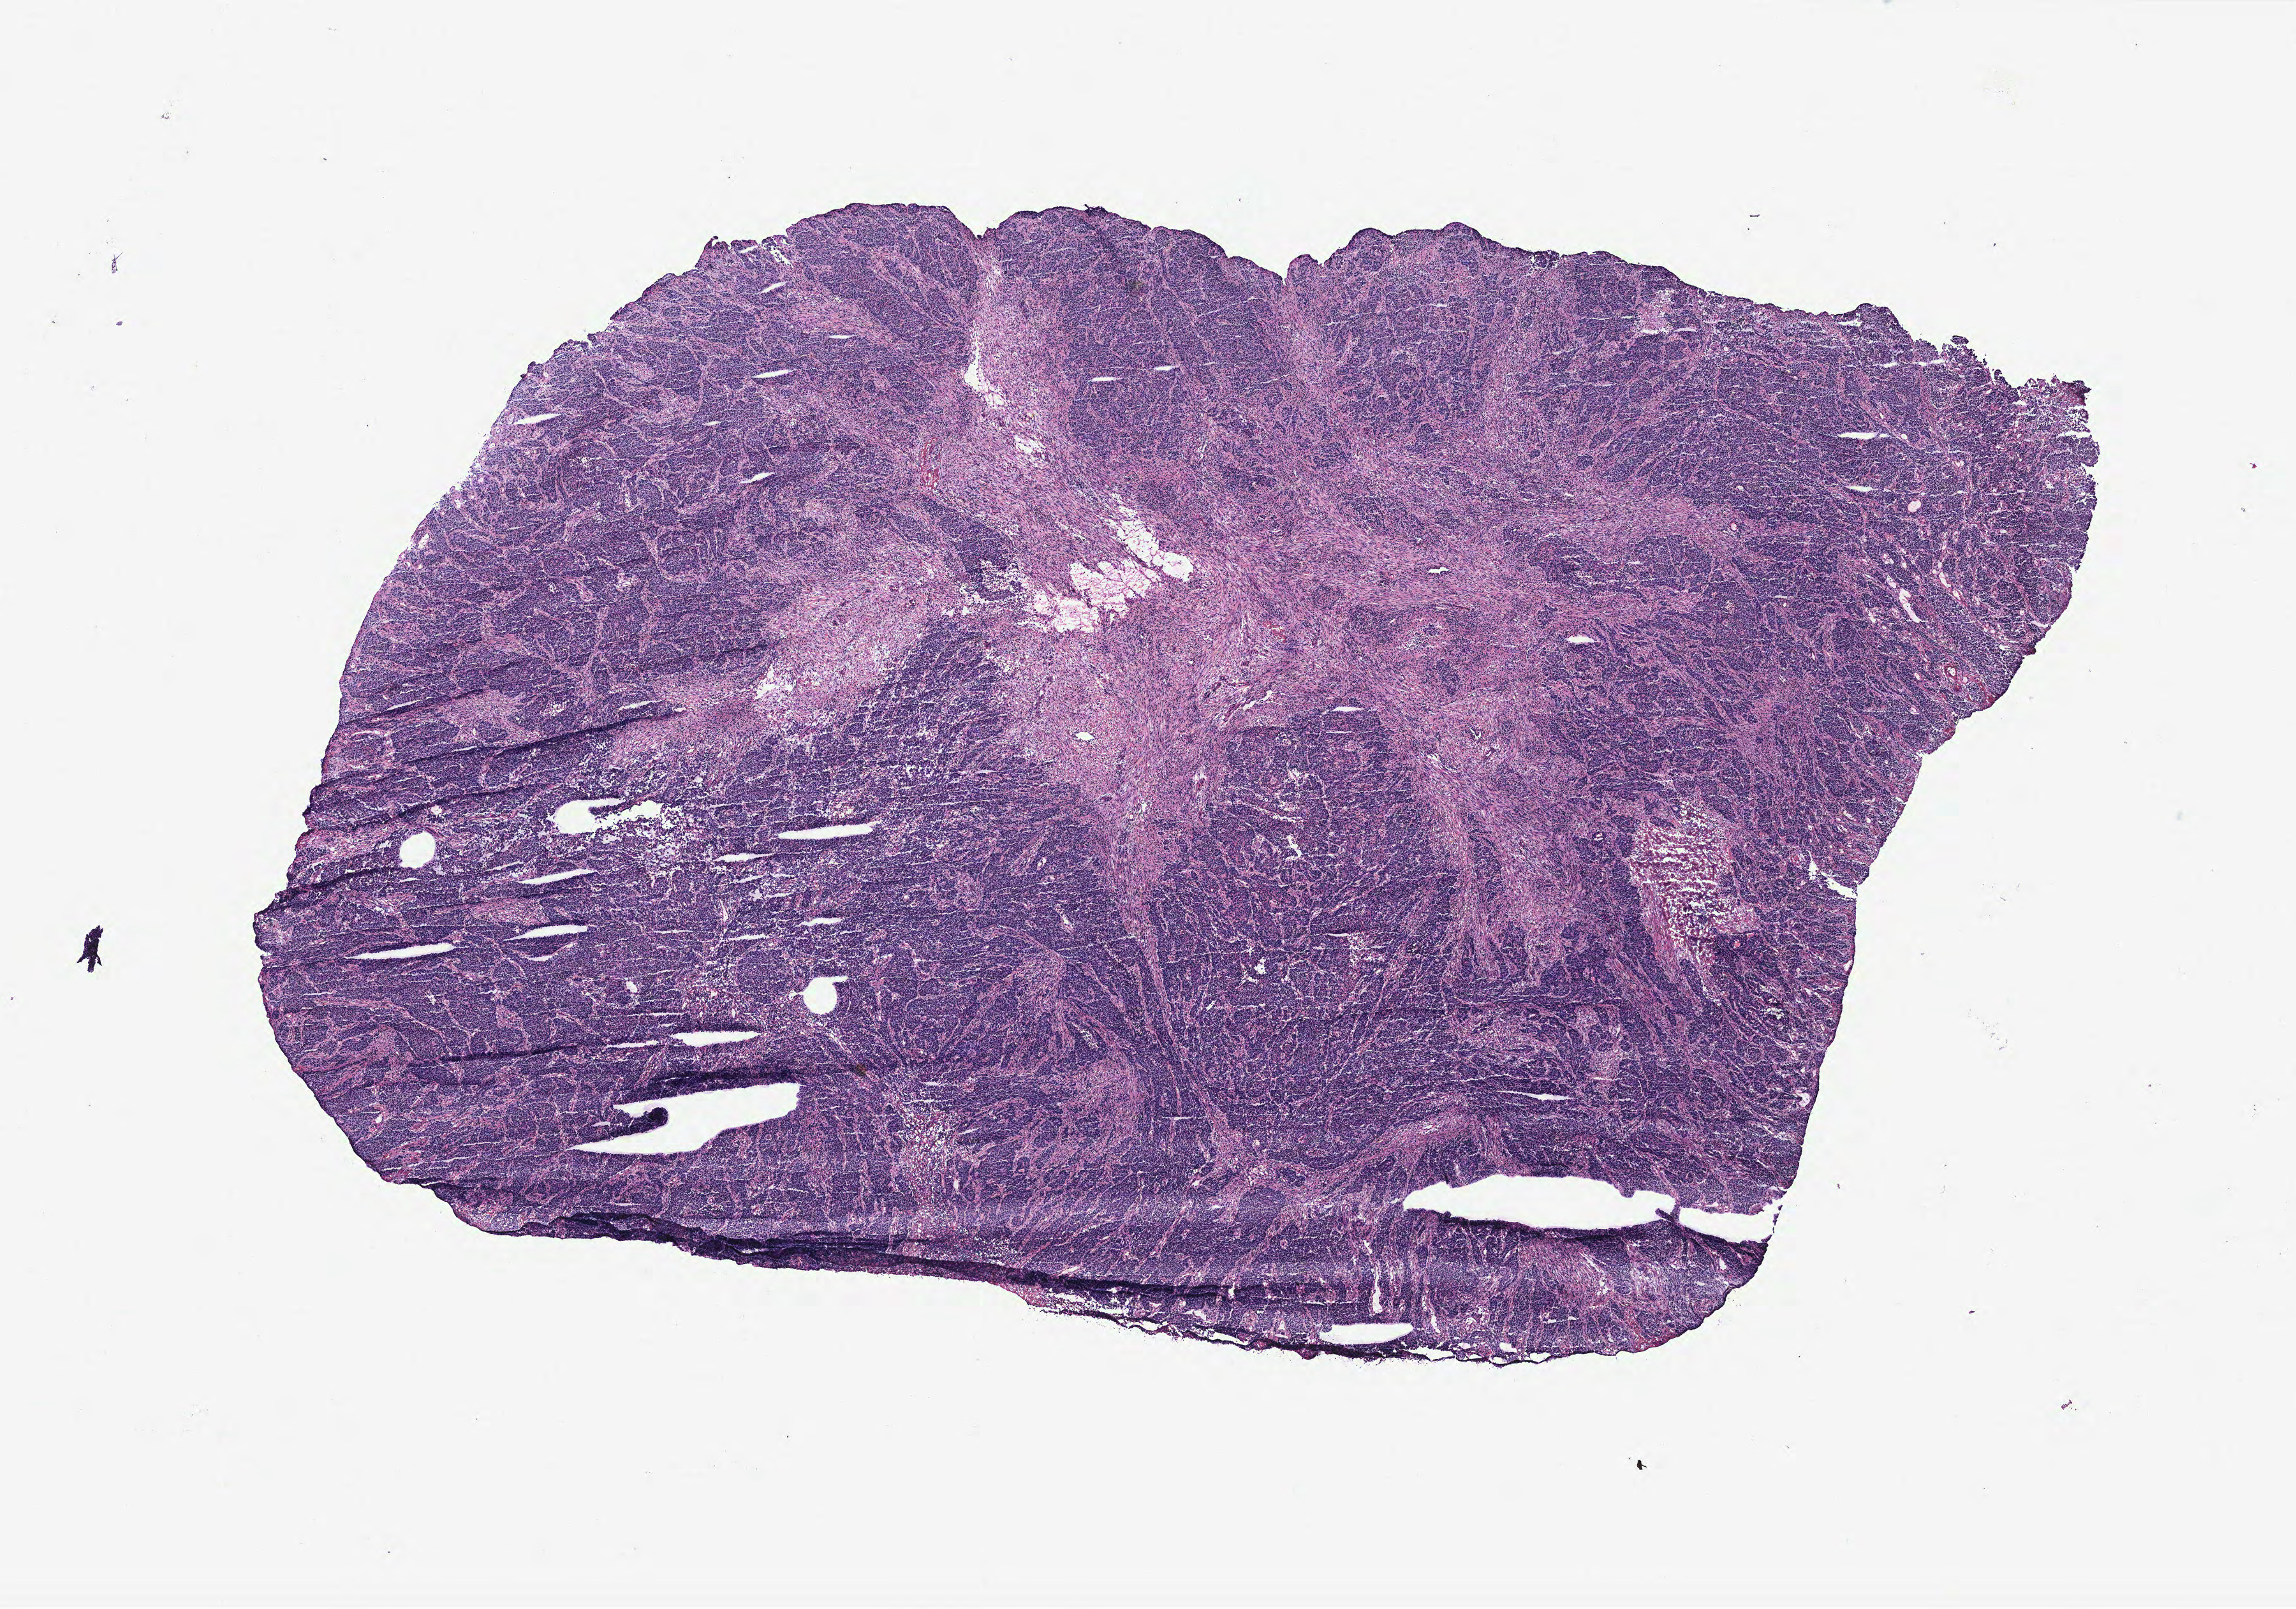
Whole-slide histology image, H&E-stained — low-resolution overview of the scanned area, about 14.4 x 10.1 mm (acquisition: 40x scan), tumour tissue sample, colon. Patient: female, age 78 years.
Primary tumour site (as recorded): colon. Histologic diagnosis: Adenocarcinoma, NOS. AJCC pathologic stage: IIA.